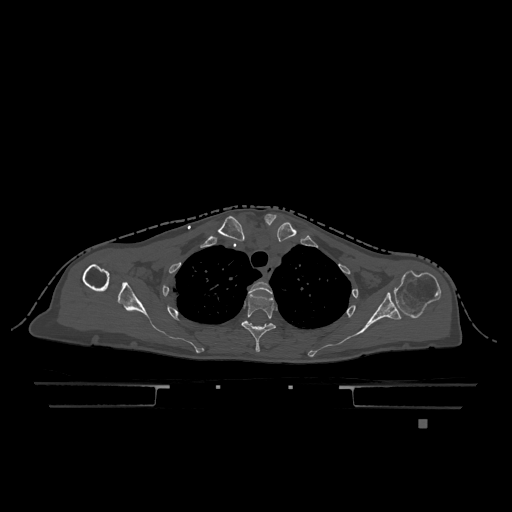
CT including the spine, one axial slice; slice 924 of 1317 in the series (ordered by position); bone window (W 1800 / L 400 HU); 0.5 mm slice thickness; 512 × 512 image matrix, field of view 500 × 500 mm. Patient: female, 74 years. Case-level facts recorded for this patient, not image findings: primary cancer: lung.
Outlined on this slice (semi-automatic segmentation, software-assisted and operator-edited):
- T2 vertebra: bounding box [x1, y1, x2, y2] px = [249, 281, 272, 294]
- T3 vertebra: [241, 294, 276, 352]
- T4 vertebra: [247, 321, 249, 323]